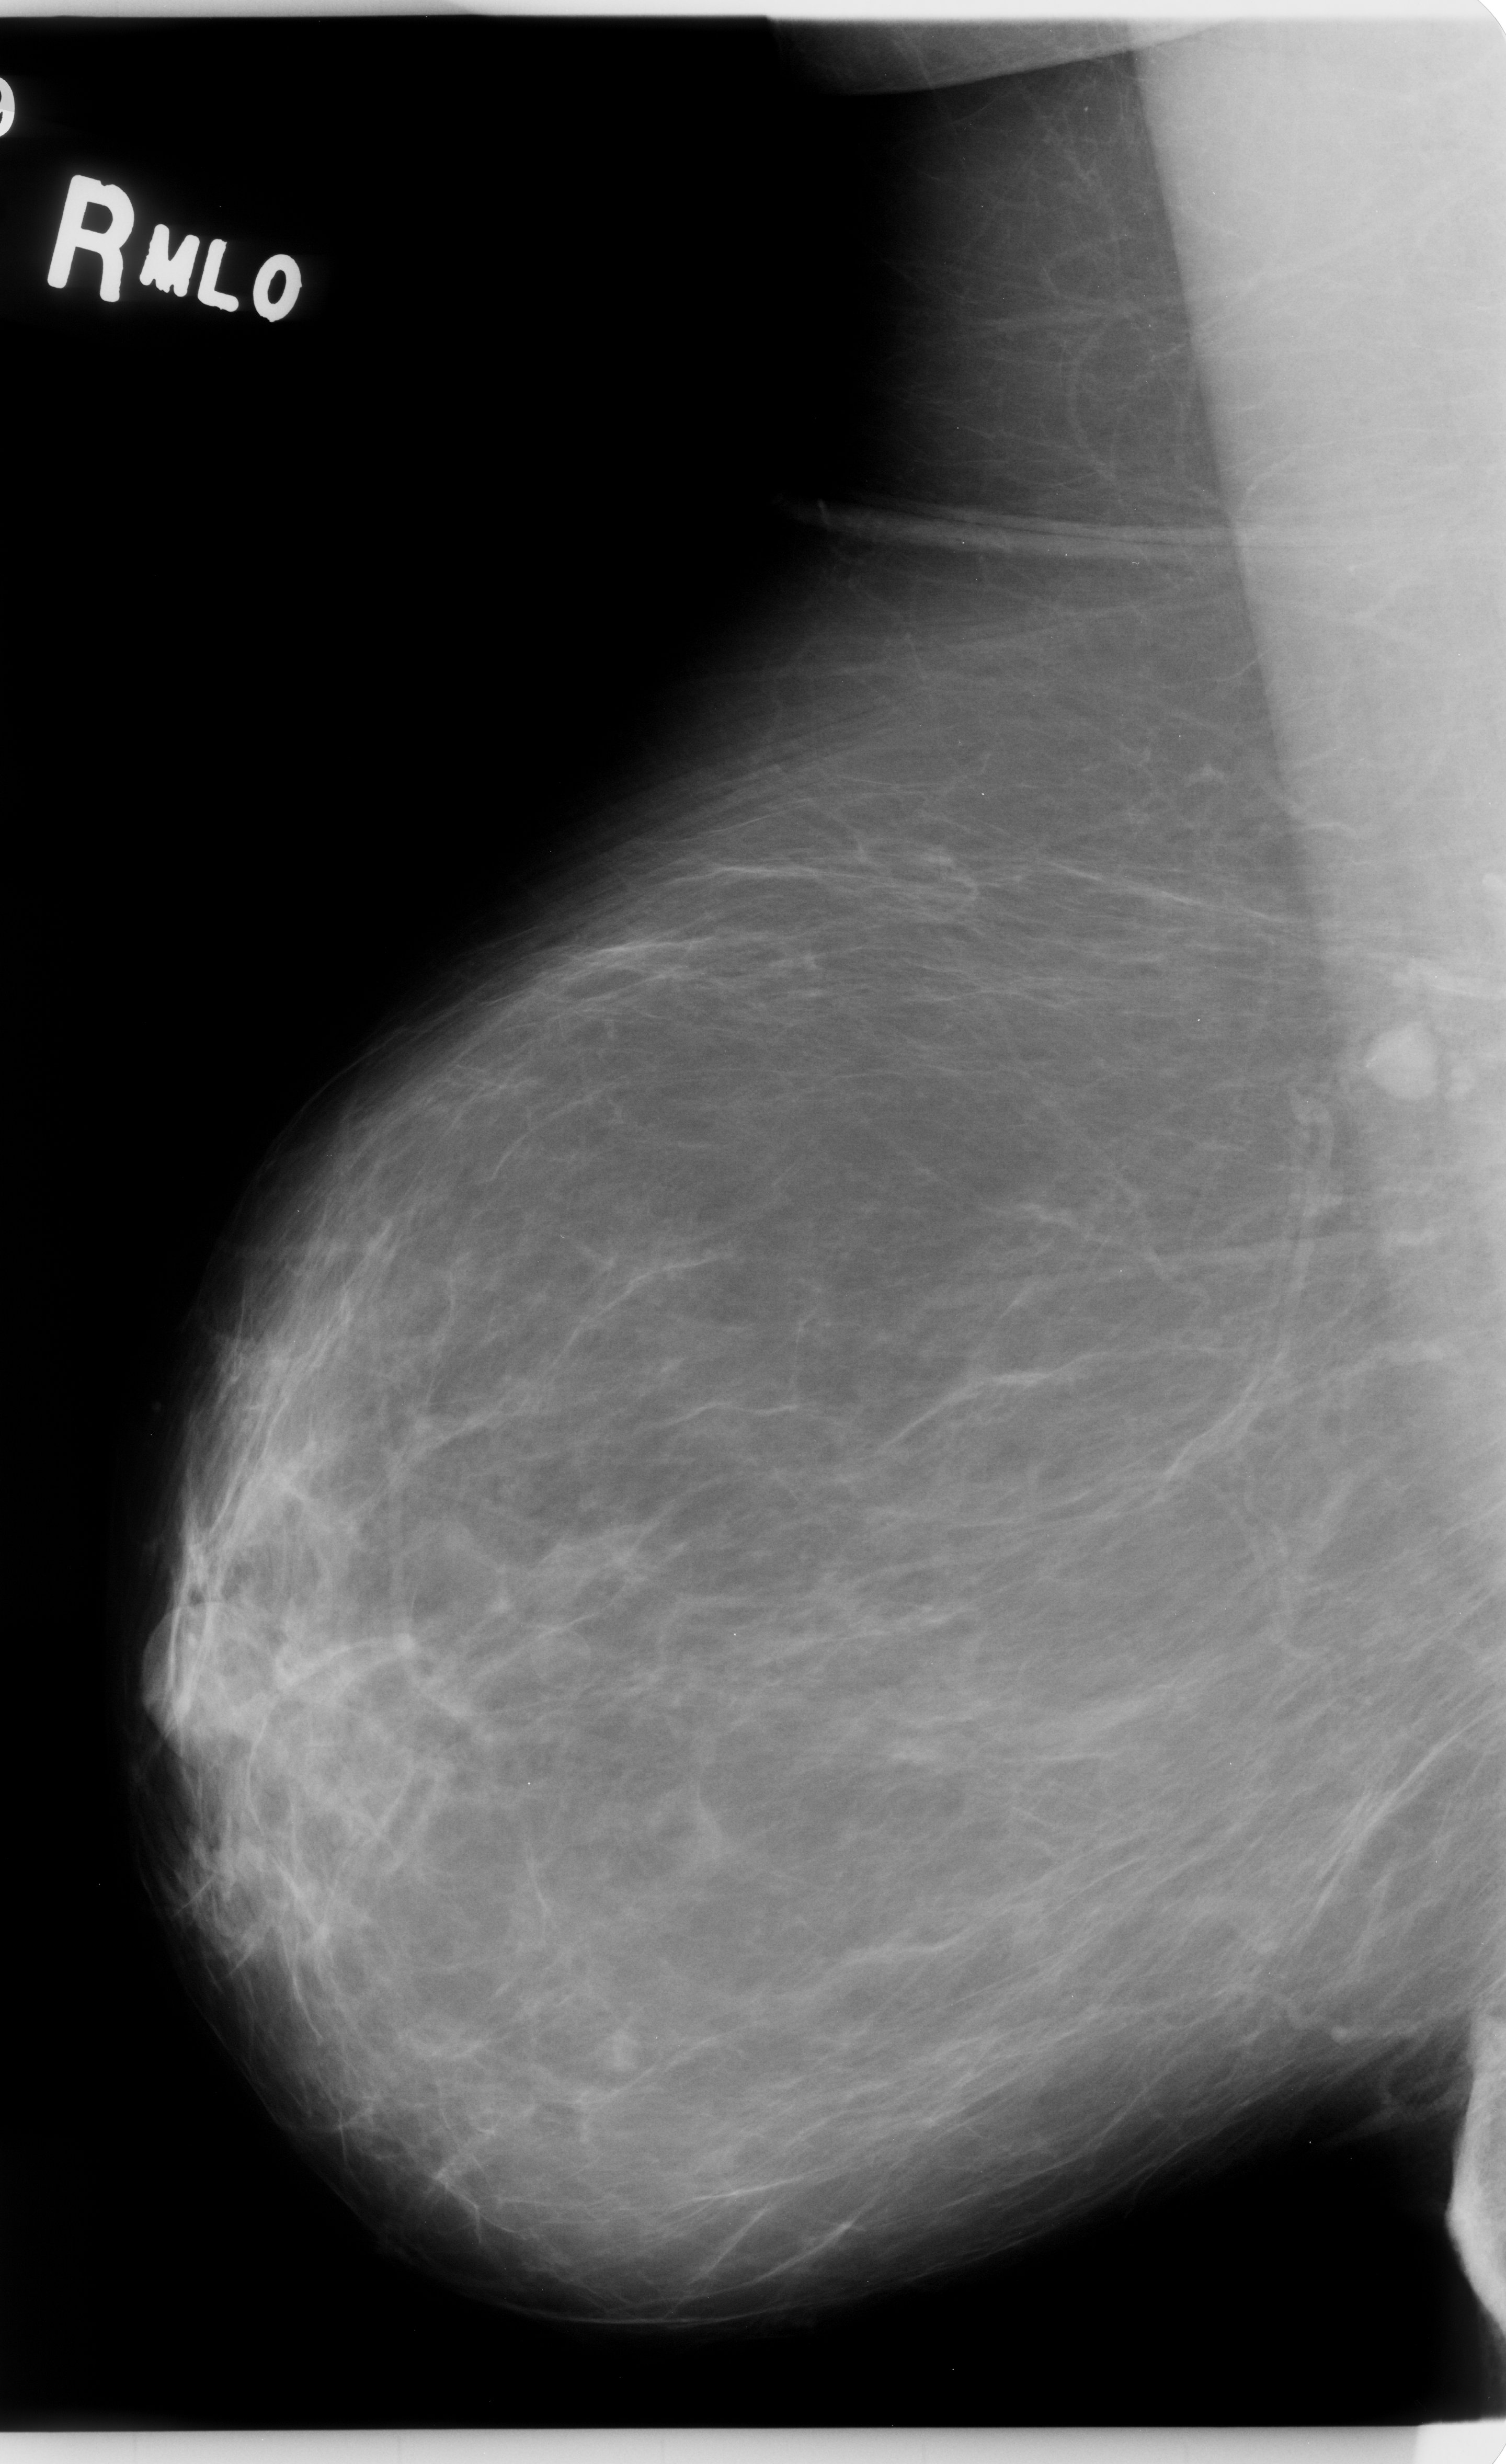
Digitized screen-film mammogram; right breast; mediolateral oblique (MLO) view; BI-RADS breast density category 1 (scale 1–4); 1506 × 2464 image matrix.
Expert-marked regions of interest on this film, with their recorded descriptors:
- mass, shape oval, margins circumscribed; BI-RADS assessment category 3; subtlety rating 5 on a 1 (subtle) to 5 (obvious) scale; pathology result (as recorded, not read from the image): benign: bounding box <1338,984,1467,1109> (left, top, right, bottom; pixels)